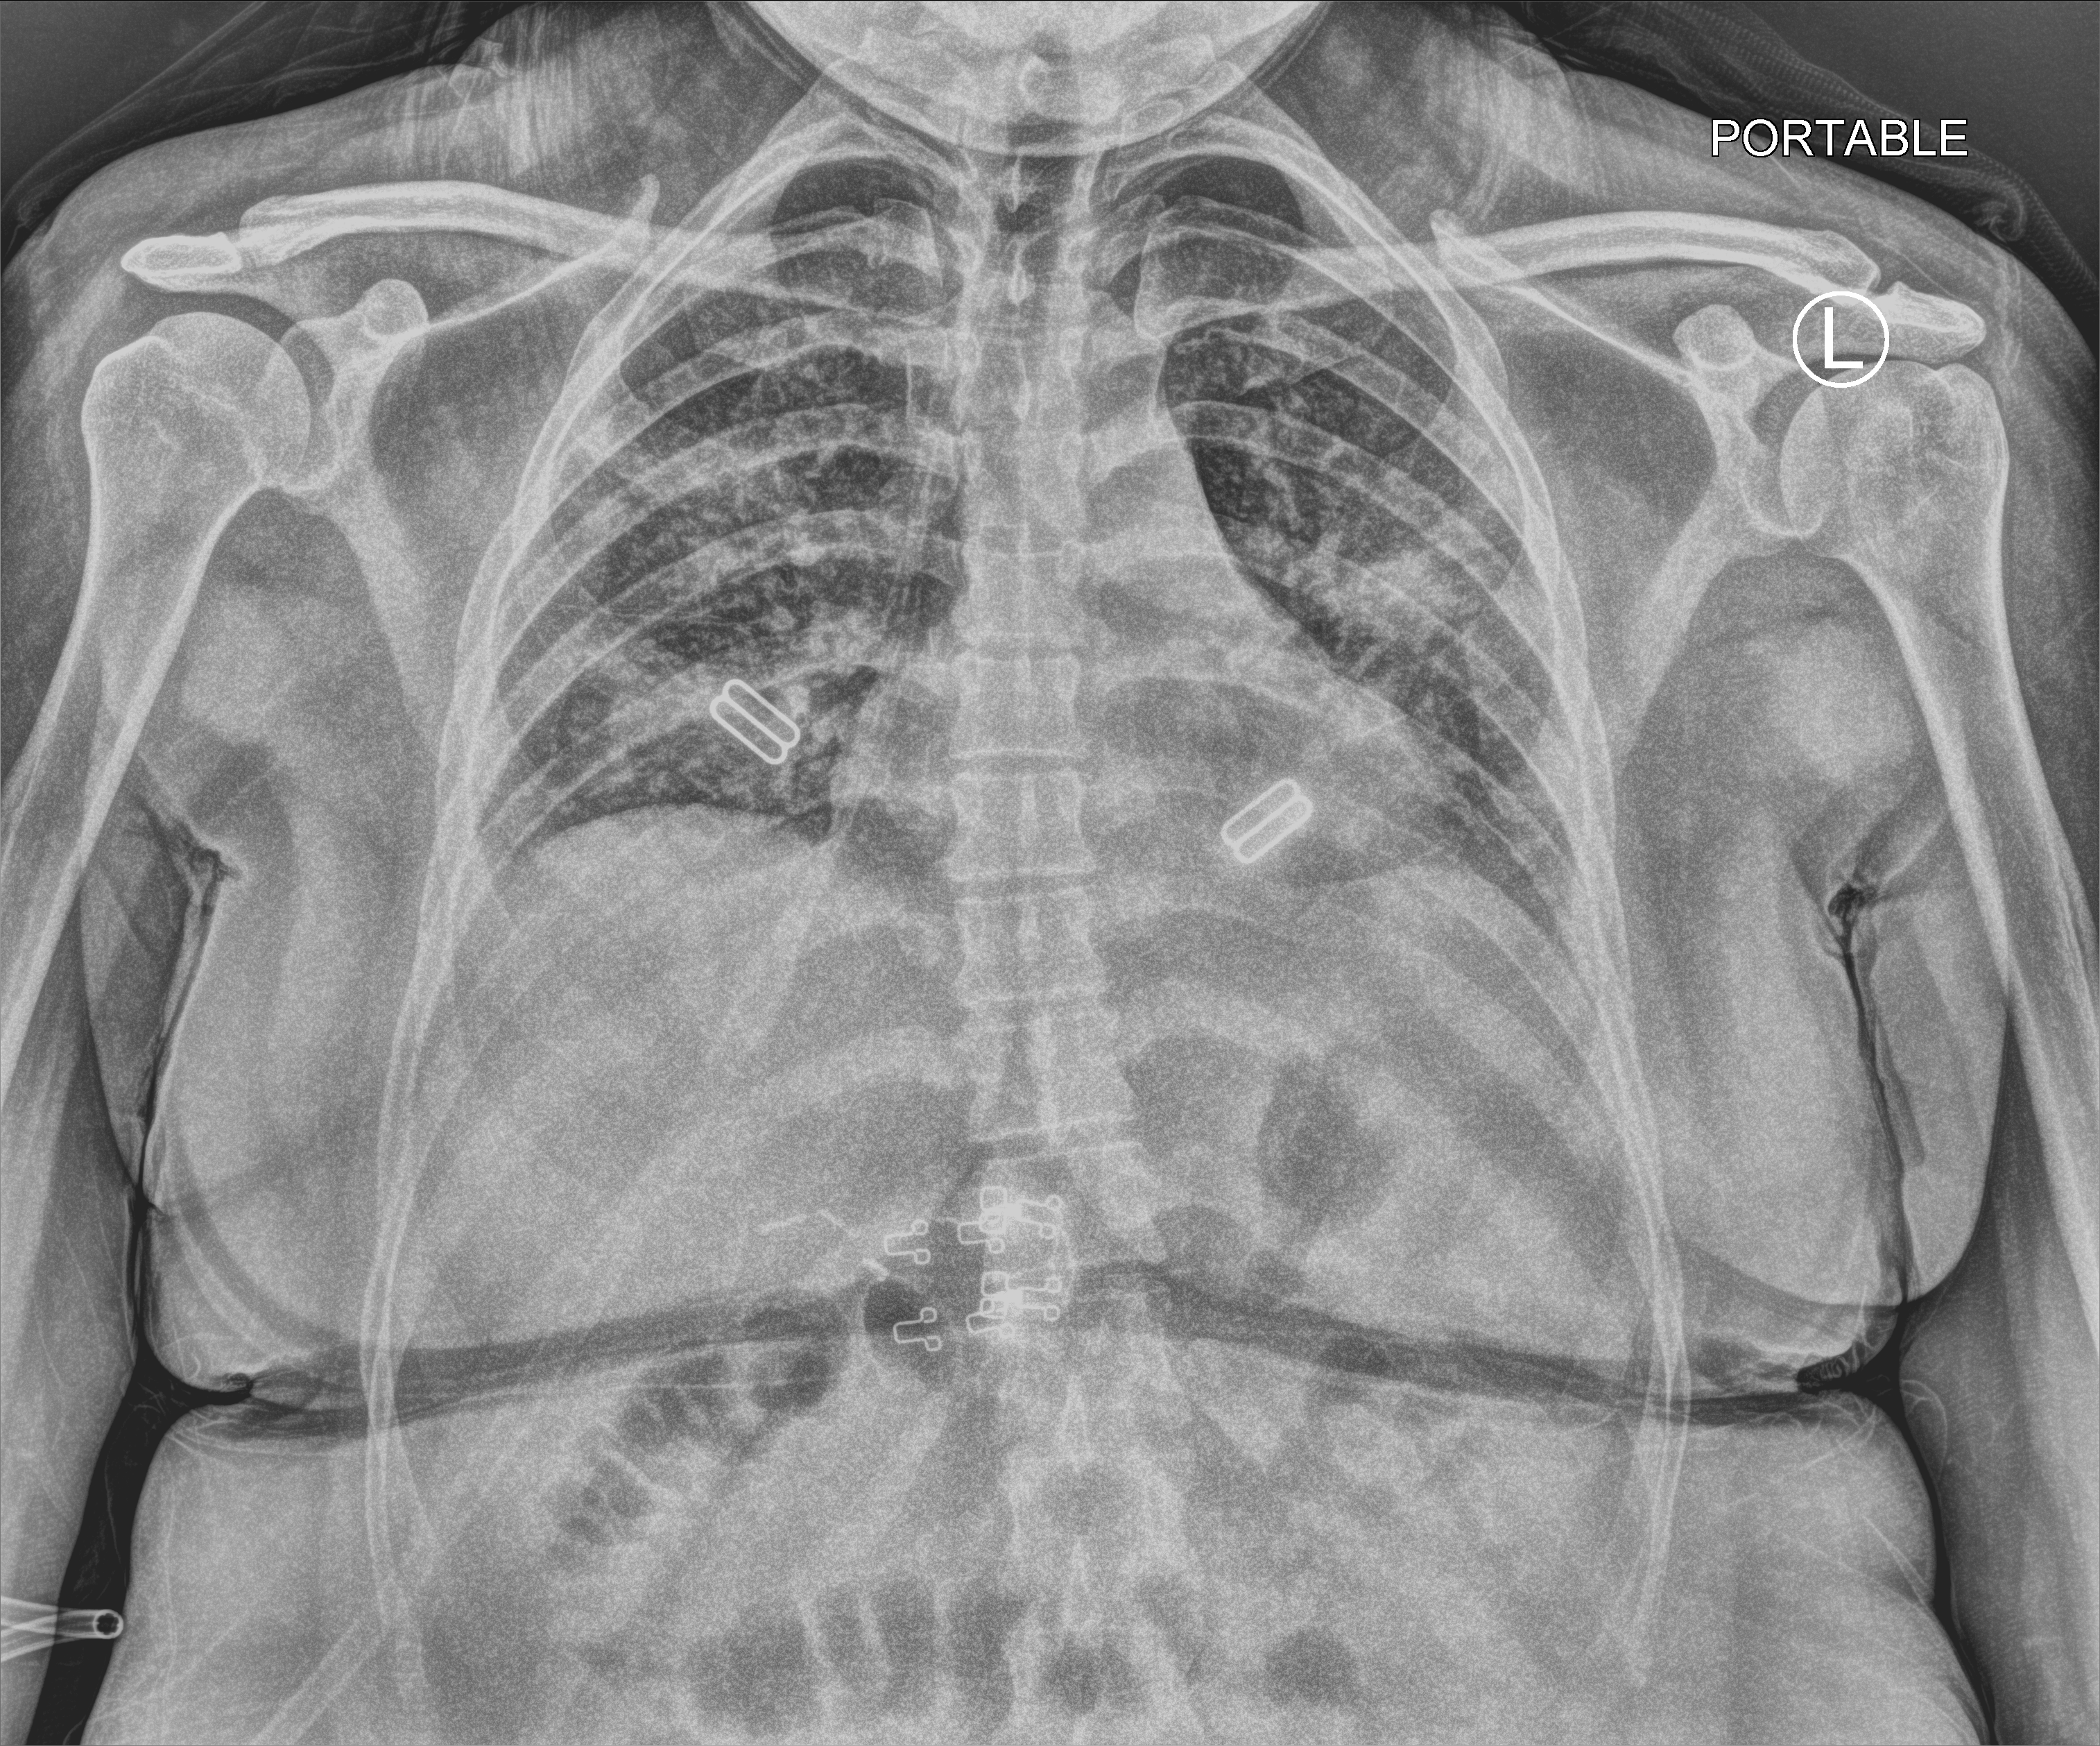
Bedside chest radiograph (computed radiography). Patient hospitalised with COVID-19; female, aged 18–59 years.
From the hospital-stay record, not from the radiograph (when in the stay this image was taken is not recorded):
- mechanically ventilated during this hospital stay: no
- COPD (admission record): no
- admitted to intensive care during this hospital stay: no